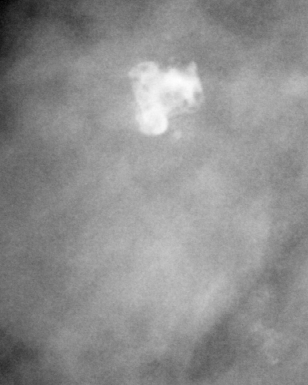
Crop from a digitized film mammogram around one marked abnormality; right breast; MLO view; BI-RADS breast density category 2 (scale 1–4).
Finding: mass, shape oval, margins microlobulated; BI-RADS assessment category 4; pathology (as recorded): benign.